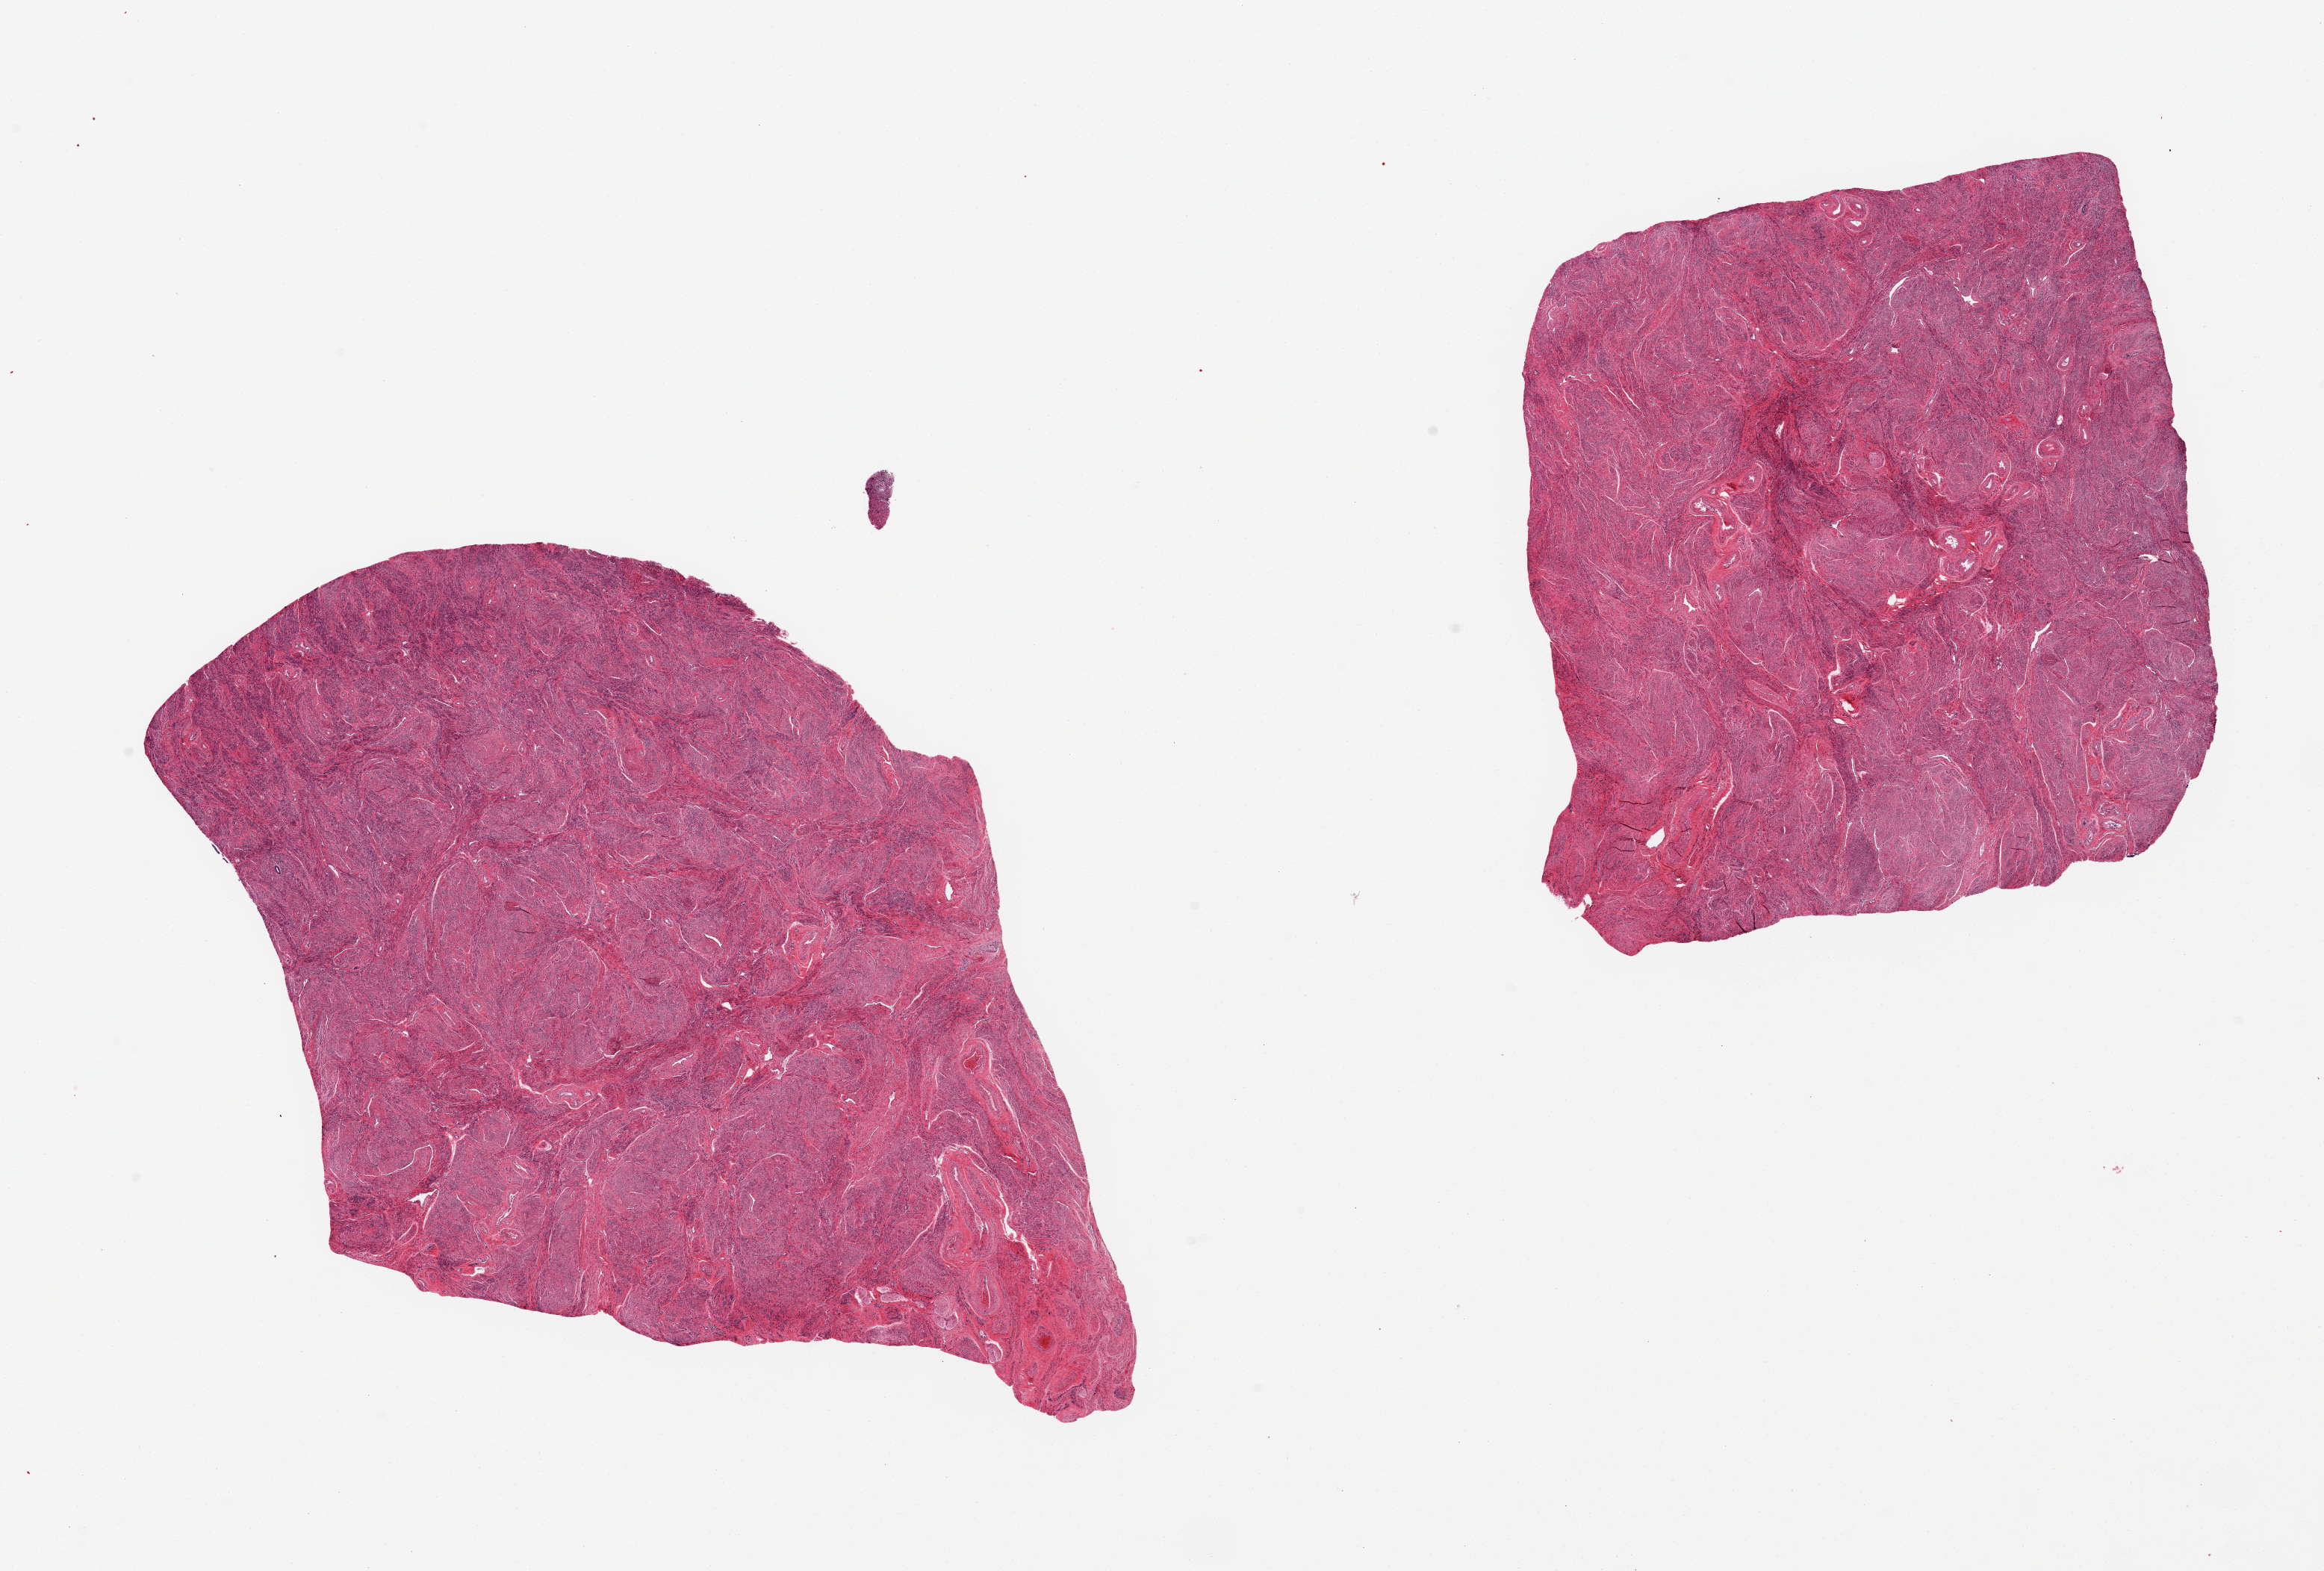
Digitized haematoxylin and eosin-stained section, brightfield, shown as a low-resolution overview of the whole scanned area (about 24.6 x 16.6 mm), PAXgene-fixed, paraffin-embedded tissue, target tissue: uterus, tissue donor sample.
Reviewer comment on this tissue sample: 2 pieces, myometrium only, no endometrium noted.